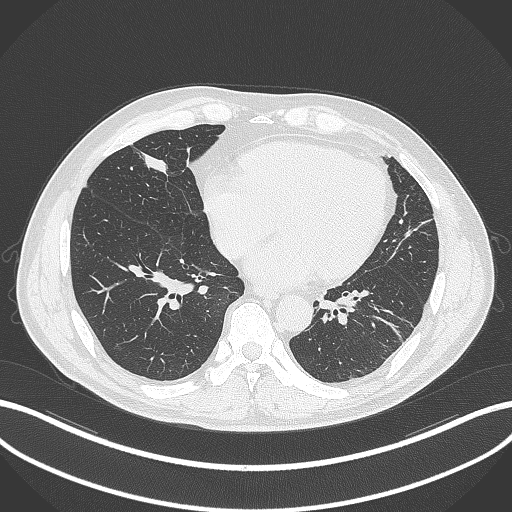
Chest CT, one axial slice. Slice 95 of 399 in the series (ordered by position). Lung window (W 1500 / L -600 HU). 1 mm slice thickness. 512 × 512 image matrix, field of view 400 × 400 mm. Patient: male, 59 years. From the clinical record (not read from this slice): clinical TNM (as recorded): T2a N1 M0.
Structures marked on this image (rectangle marked by the reading radiologist):
- lung tumour (recorded histology: adenocarcinoma): box from (x=132, y=144) to (x=170, y=181) px